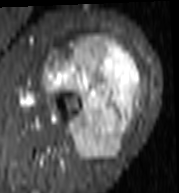
MRI of an extremity soft-tissue mass, one axial slice. Position 62 of 103 along the scan axis. STIR. MR volume resampled by the dataset authors to the PET/CT grid (not the native acquisition matrix). 3.27 mm slice thickness. 179 × 193 image matrix, field of view 175 × 188 mm. Female patient. From the clinical record (not read from this slice): histological type: undifferentiated – high grade; grade: high; site of the primary tumour: left thigh.
Annotated regions visible in this slice (expert contour drawn on MRI and transferred to this co-registered scan by the dataset authors):
- gross tumour volume including surrounding oedema: bounding box [x1, y1, x2, y2] px = [43, 35, 142, 161]
- gross tumour volume (mass): [43, 35, 142, 161]